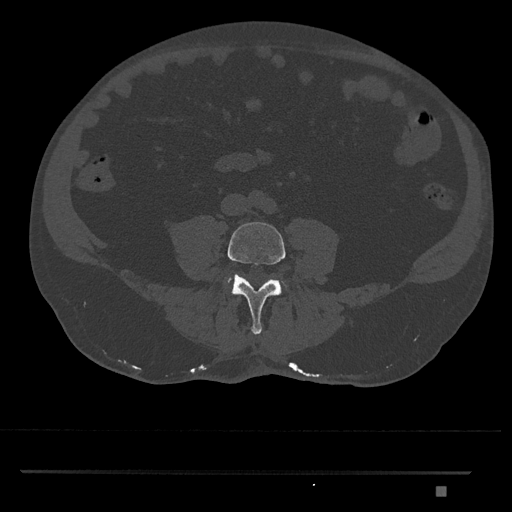
CT including the spine, one axial slice. Position 607 of 1134 along the scan axis. Reconstruction kernel Br40s/3. 120 kVp. Bone window (W 1800 / L 400 HU). 0.5 mm slice thickness. 512 × 512 image matrix. Male patient, age 65 years. Case-level facts recorded for this patient, not image findings: primary cancer: prostate.
Outlined on this slice (semi-automatically segmented with operator editing):
- L4 vertebra: bounding box (x1, y1, x2, y2) in pixels: (226, 222, 286, 335)